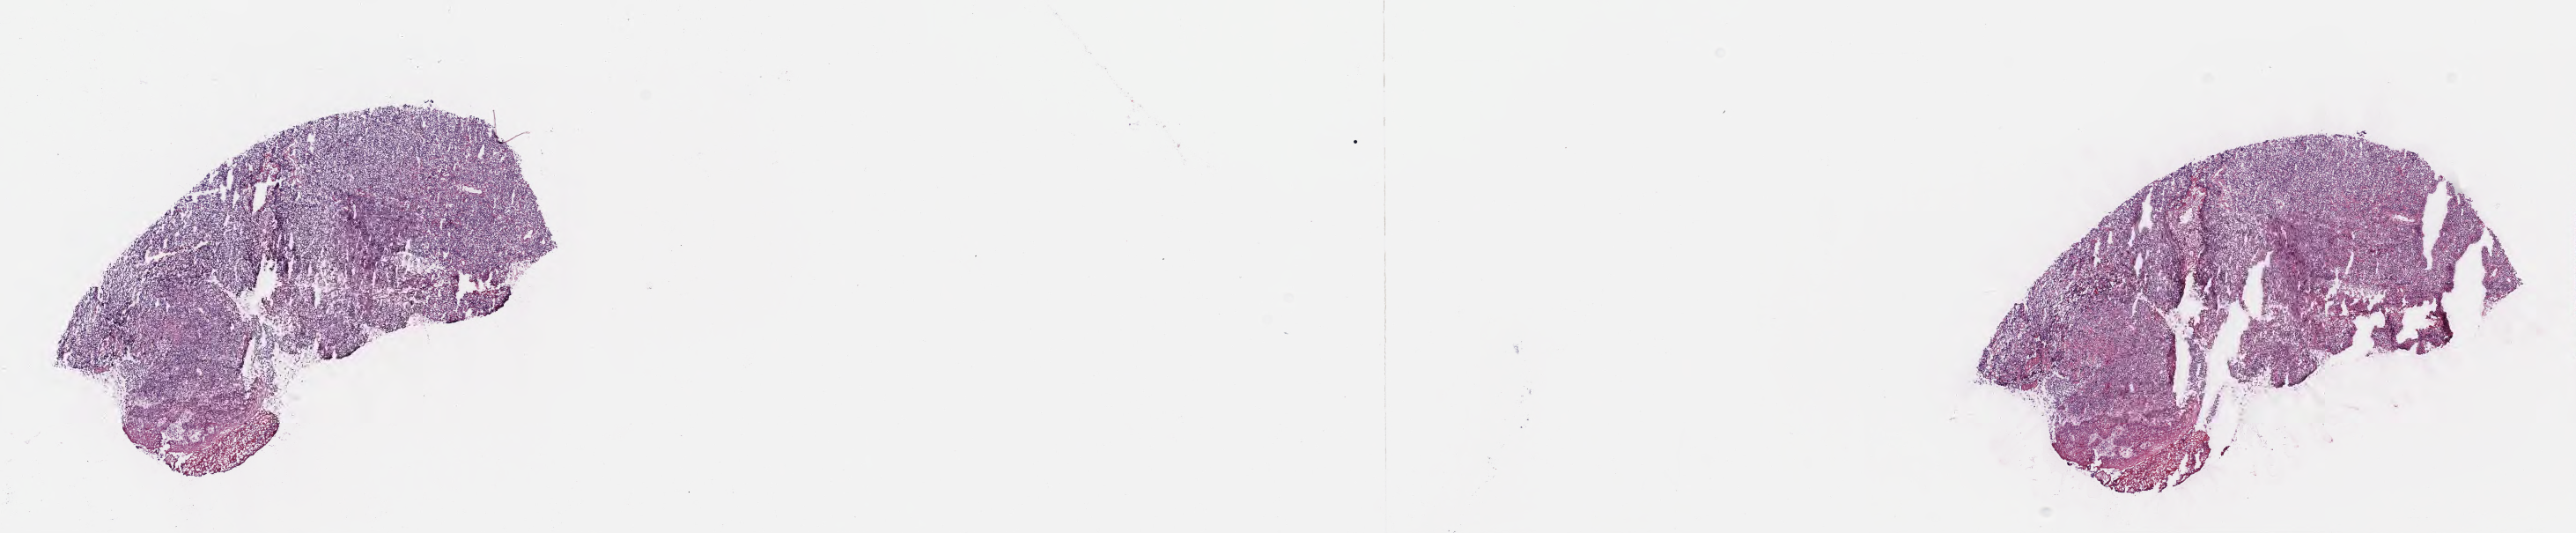
Whole-slide image, hematoxylin and eosin (H&E) stain — low-resolution overview of the scanned area, about 23.6 x 4.9 mm; frozen section; primary tumor; site: cranium. Female patient; age at initial diagnosis 5 years. Pathologist review of this section (percent, as recorded): tumor cells 90%, tumor nuclei 90%, stromal cells 7%, necrosis 3%, normal cells 0%. Inflammatory infiltration, as recorded: lymphocyte infiltration 80%, monocyte infiltration 10%, neutrophil infiltration 0%.
Section: bottom of the tissue portion. Ann Arbor stage (patient): Stage I. Diagnosis: Burkitt lymphoma, NOS.